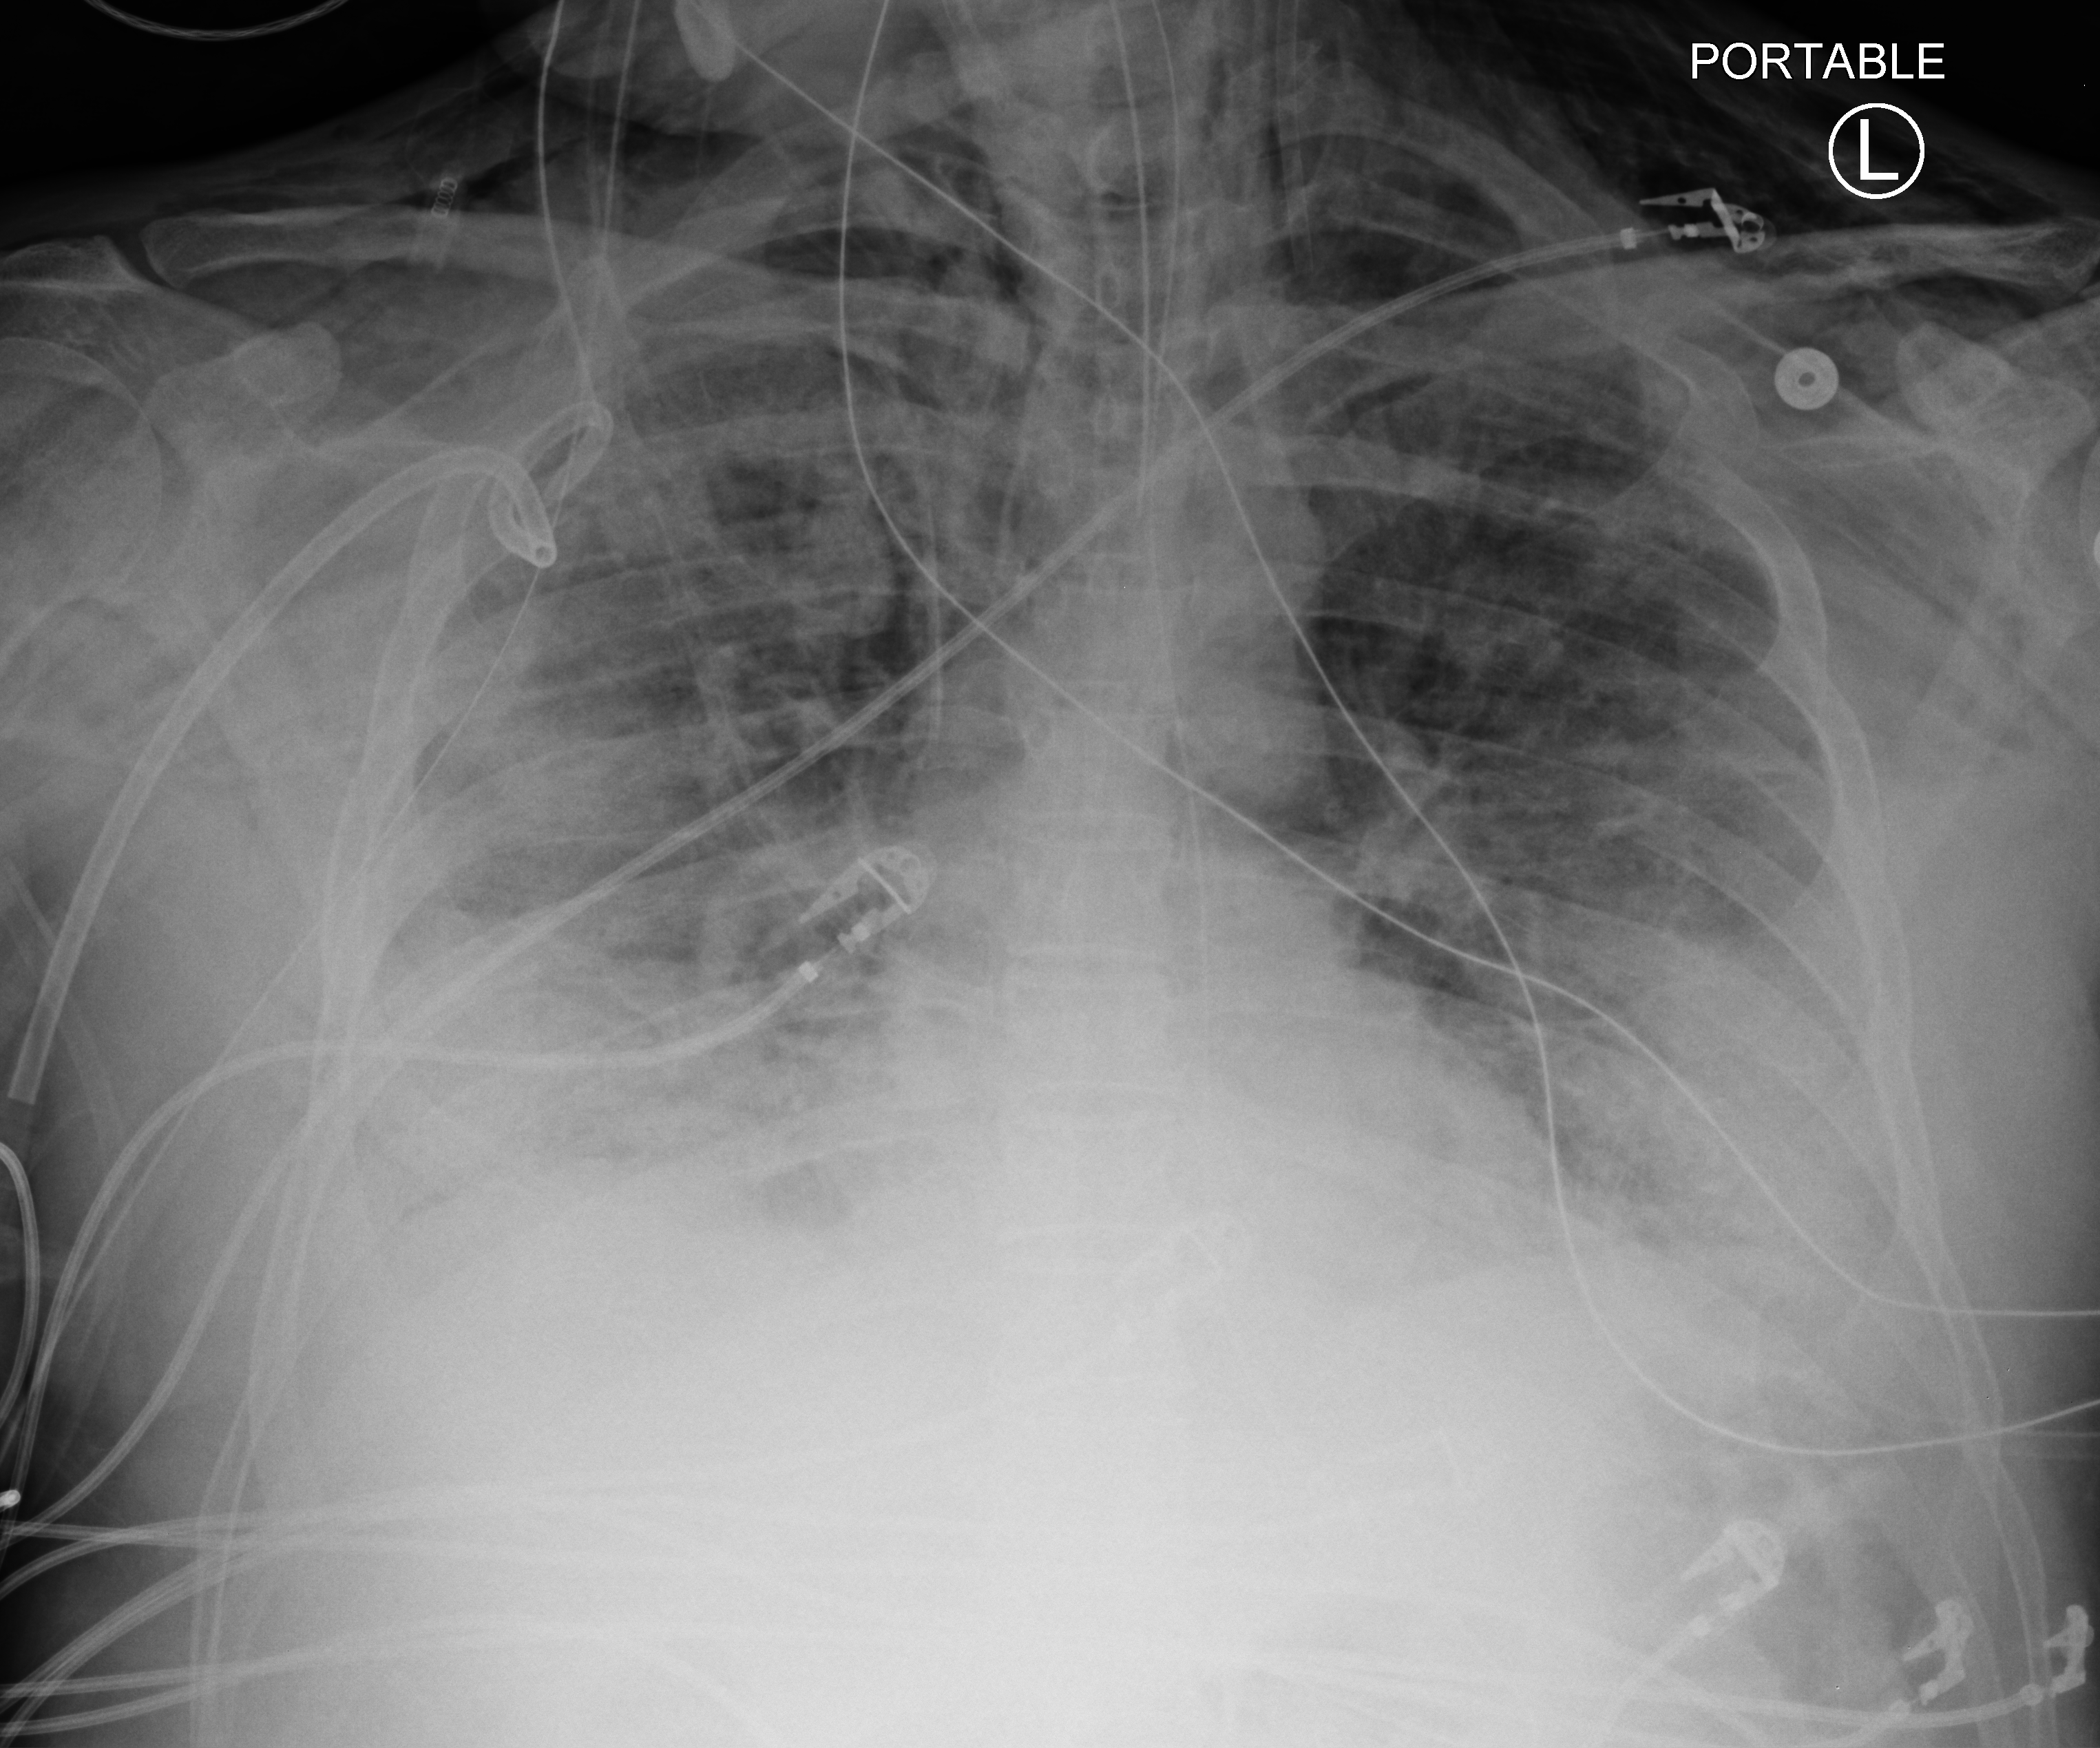
Portable chest radiograph; anteroposterior (AP) projection. Patient hospitalised with COVID-19; male, aged 60–74 years.
From the hospital-stay record, not from the radiograph (when in the stay this image was taken is not recorded):
- chronic kidney disease (admission record): no